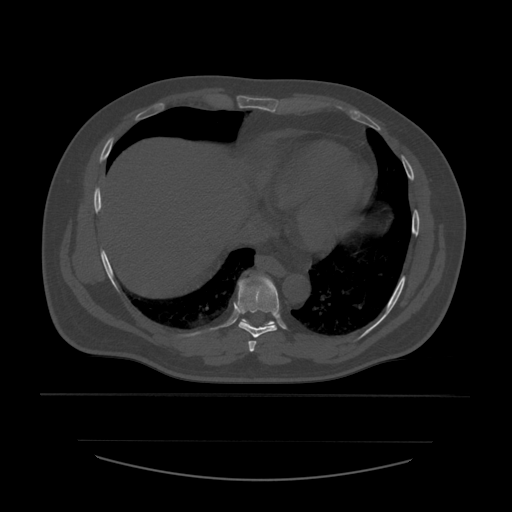
CT including the spine, one axial slice; slice 333 of 532 in the series (ordered by position); reconstruction kernel STANDARD; bone window (W 1800 / L 400 HU); 1.25 mm slice thickness; 512 × 512 image matrix. Patient age 44 years. Case-level facts recorded for this patient, not image findings: primary cancer: soft tissue sarcoma.
Outlined on this slice (semi-automatically segmented with operator editing):
- T7 vertebra: bounding box <248,341,257,353> (left, top, right, bottom; pixels)
- T8 vertebra: <235,276,280,338>
- T9 vertebra: <242,280,278,328>